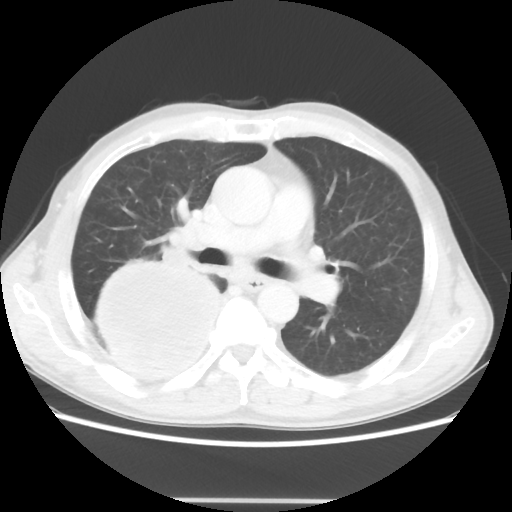
Chest CT, one axial slice; position 29 of 48 along the scan axis; 100 kVp; lung window (W 1500 / L -600 HU); 512 × 512 image matrix, field of view 361 × 361 mm. Male patient, age 66 years. From the clinical record (not read from this slice): clinical TNM (as recorded): T4 N1 M1.
Outlined on this slice (rectangle marked by the reading radiologist):
- lung tumour (recorded histology: small cell carcinoma): box from (x=94, y=260) to (x=222, y=383) px